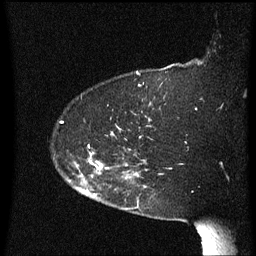
Breast MRI (dynamic contrast-enhanced), one sagittal slice. Slice 49 of 60 in the series (ordered by position). Dynamic contrast-enhanced series, image 2 of 3 at this slice position (ordered by acquisition). 1.5 T. TE 4.2 ms, TR 8.4 ms. 2.3 mm slice thickness. 256 × 256 image matrix, field of view 200 × 200 mm. Patient: female, 63 years. Case-level facts recorded for this patient, not image findings: setting: breast cancer imaged before/during neoadjuvant chemotherapy; receptor status: HER2-positive.
Annotated regions visible in this slice (semi-automatic segmentation, software-assisted and operator-edited):
- analysis volume of interest (the breast-tissue region the enhancement analysis was run in; not a lesion): bounding box [x1, y1, x2, y2] px = [71, 150, 147, 207]
- tumour enhancement mask (voxels above the 70 % enhancement threshold inside the analysis volume of interest): [90, 158, 103, 171]